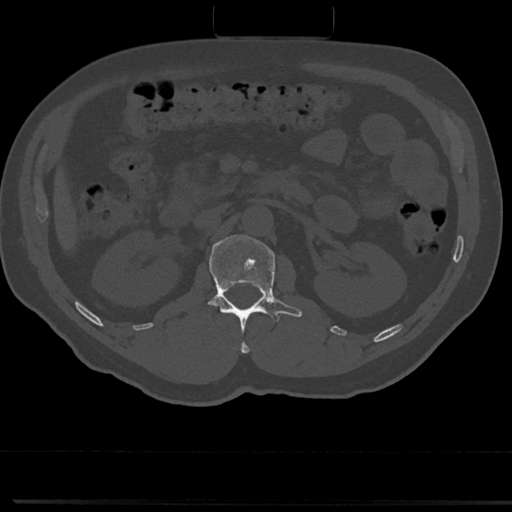
CT including the spine, one axial slice. Position 77 of 817 along the scan axis. 120 kVp. Bone window (W 1800 / L 400 HU). 0.5 mm slice thickness. 512 × 512 image matrix, field of view 355 × 355 mm. Patient: male, 61 years. From the clinical record (not read from this slice): primary cancer: prostate.
Annotated regions visible in this slice (semi-automatically segmented with operator editing):
- L1 vertebra: box from (x=191, y=236) to (x=301, y=350) px